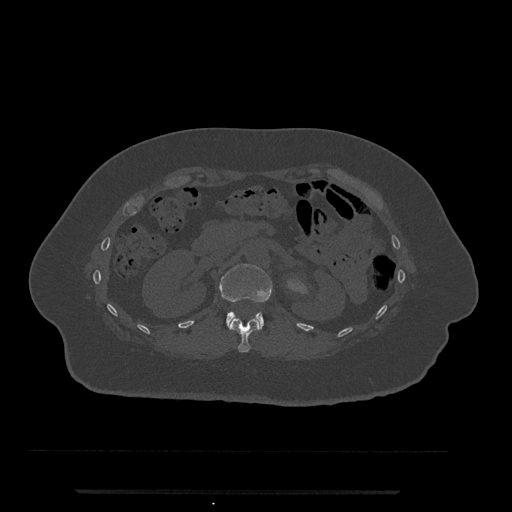
CT including the spine, one axial slice. Slice 134 of 797 in the series (ordered by position). Reconstruction kernel Br40s/3. 120 kVp. Bone window (W 1800 / L 400 HU). 512 × 512 image matrix, field of view 440 × 440 mm. Patient: female, 51 years. From the clinical record (not read from this slice): primary cancer: neuro; vertebrae with lytic lesions (as recorded): T8.
Outlined on this slice (semi-automatically segmented with operator editing):
- L1 vertebra: bounding box [x1, y1, x2, y2] px = [219, 264, 273, 330]
- T12 vertebra: [229, 317, 259, 353]